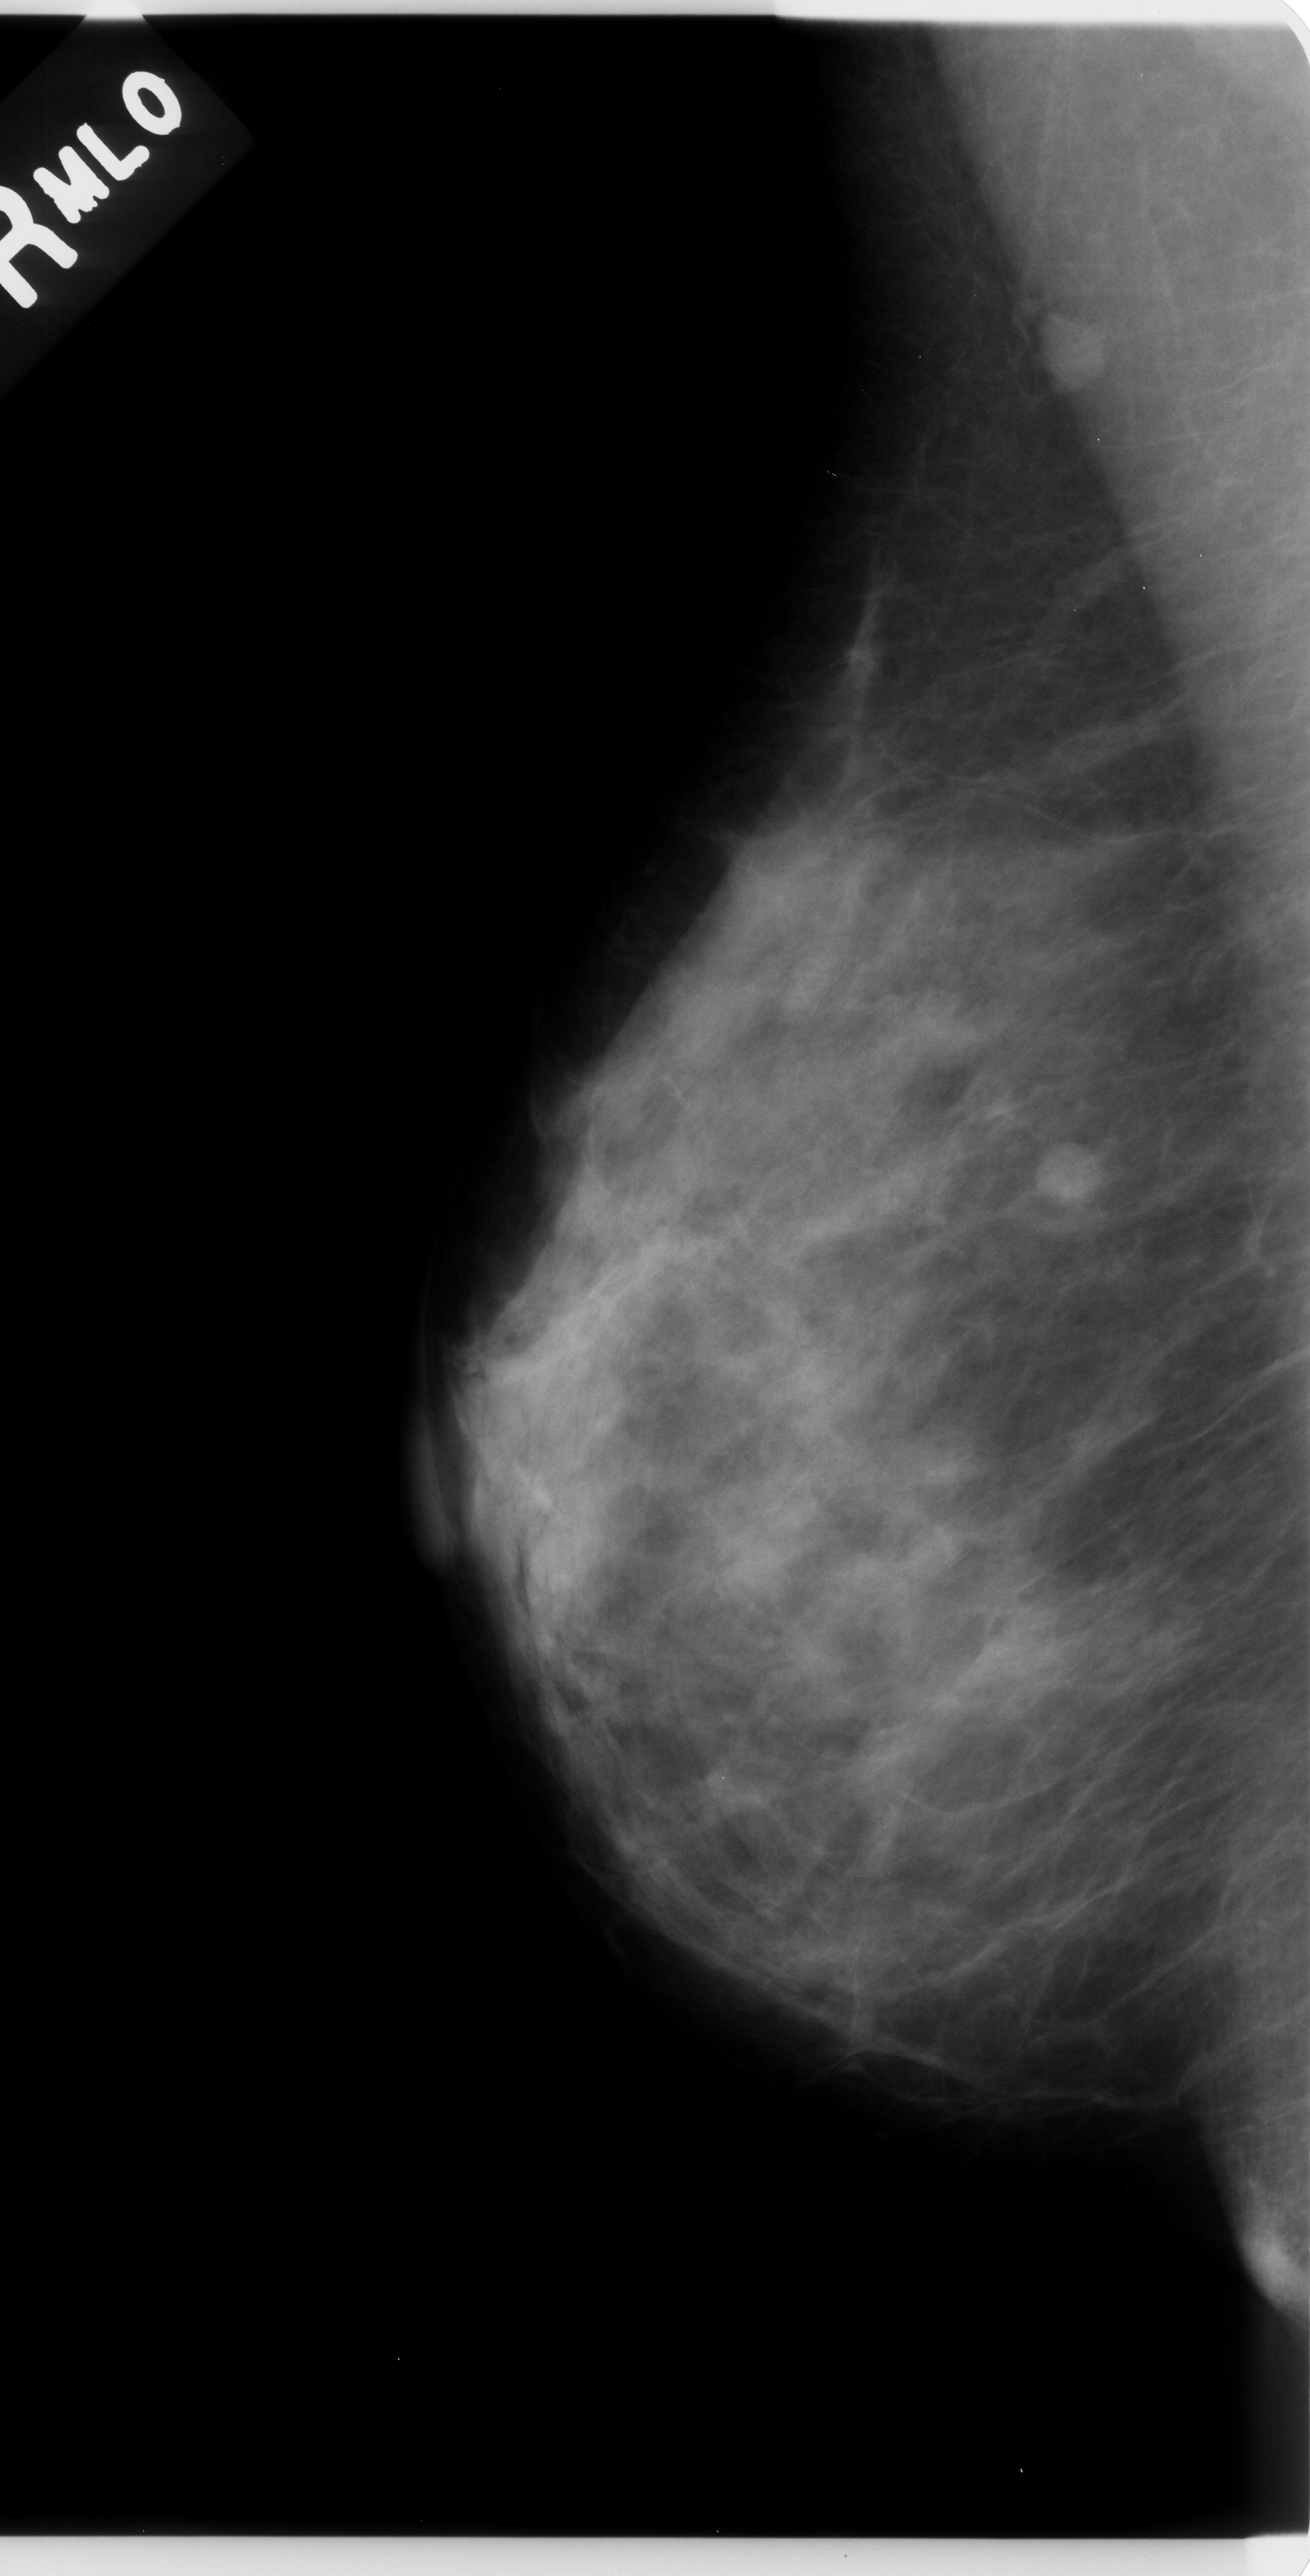
Digitized screen-film mammogram. Right breast. MLO view. 1310 × 2576 image matrix.
Expert-marked regions of interest on this image (one box per marked abnormality):
- Finding 1 of 2: mass, shape round, margins circumscribed; BI-RADS assessment category 4; pathology (as recorded): malignant: bounding box (x1, y1, x2, y2) in pixels: (1012, 1127, 1129, 1240)
- Finding 2 of 2: mass, shape round, margins circumscribed; BI-RADS assessment category 4; pathology result (as recorded, not read from the image): malignant: (1030, 292, 1122, 398)